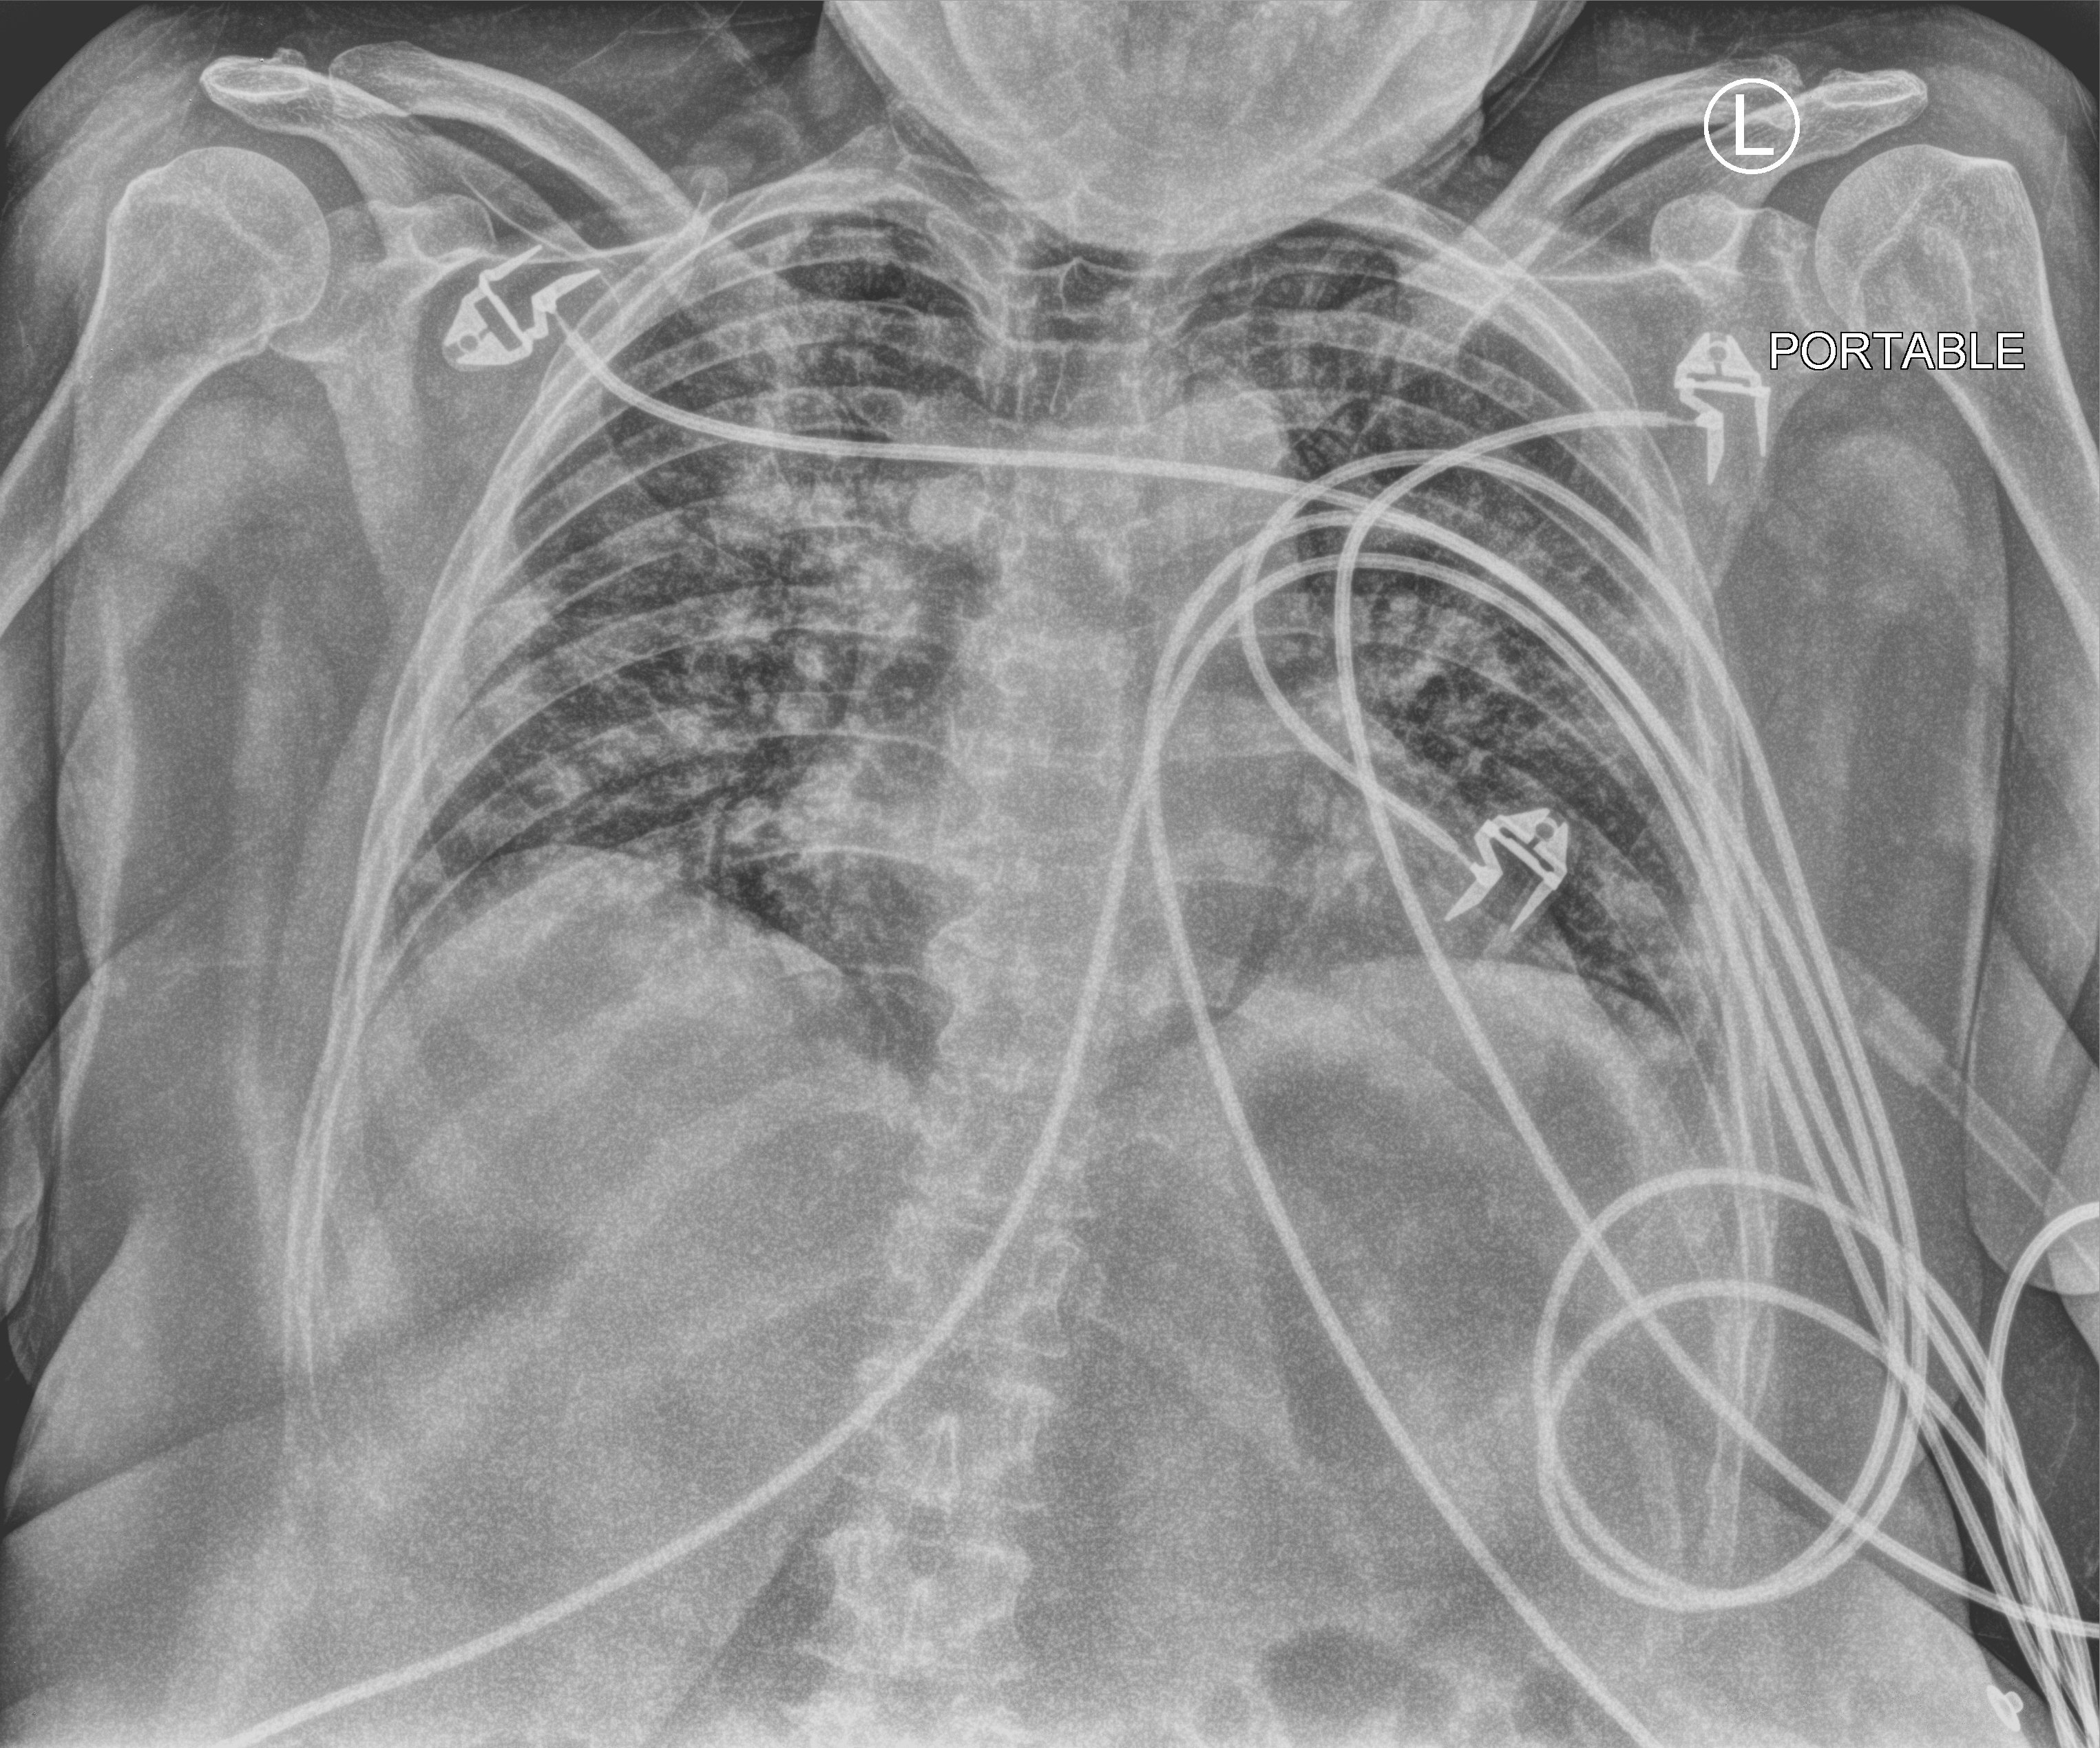
Bedside chest radiograph (computed radiography), anteroposterior (AP) projection. Patient hospitalised with COVID-19; female, aged 18–59 years.
Admission-level facts for this patient (not findings on this image; timing relative to this image not recorded):
- admitted to intensive care during this hospital stay: yes
- mechanically ventilated during this hospital stay: no